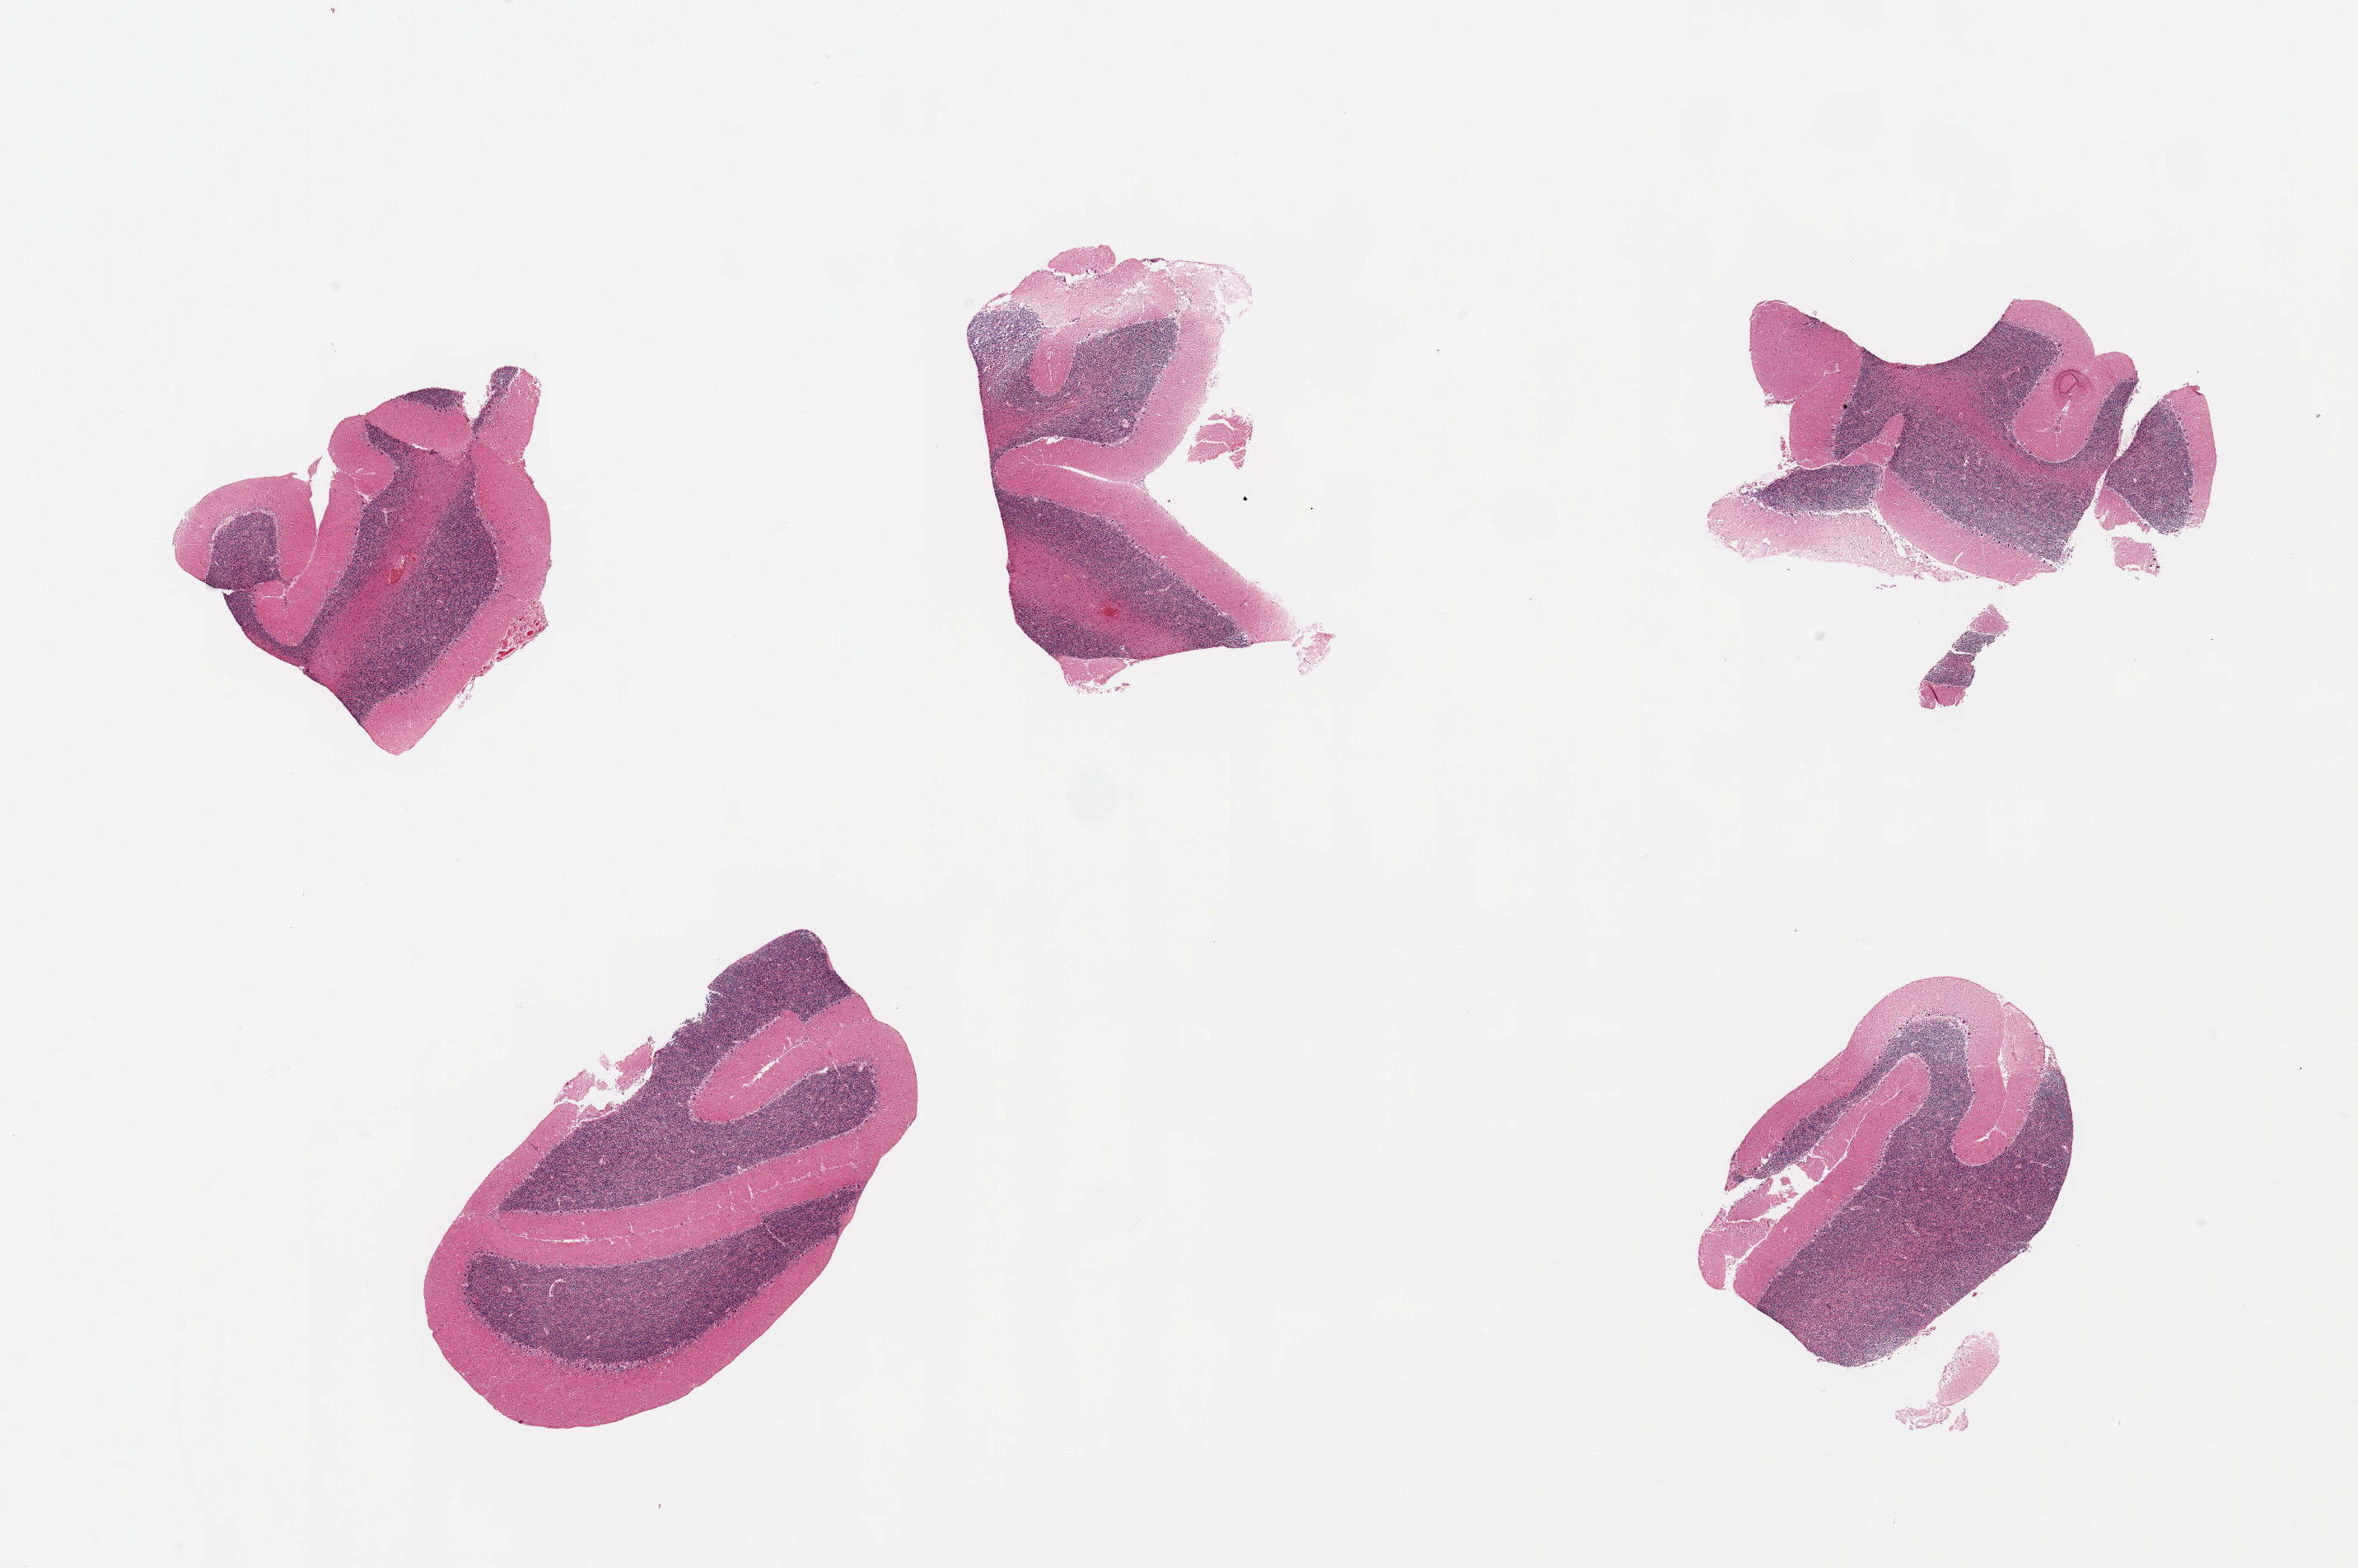
Whole-slide image, haematoxylin and eosin stain, brightfield, low-resolution overview of the scanned area, about 22.6 x 15.1 mm (acquisition: 20x scan), PAXgene-fixed, paraffin-embedded tissue, section of cerebellum (target tissue), donor tissue sample. Donor sex: male.
• pathologist's review note for this sample: 5 pieces, no abnormalities